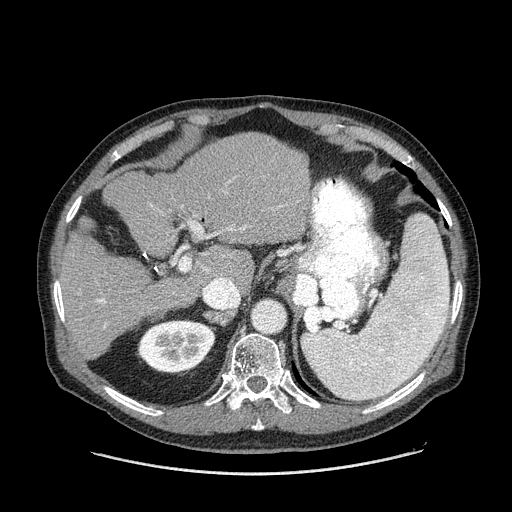
Contrast-enhanced abdominal CT (liver protocol), one axial slice. Slice 94 of 180 in the series (ordered by position). Reconstruction kernel STANDARD. 120 kVp. One of 2 acquisitions stored at this slice position. Soft-tissue window (W 400 / L 40 HU). 2.5 mm slice thickness. 512 × 512 image matrix, field of view 420 × 420 mm. Case-level facts recorded for this patient, not image findings: diagnosis: hepatocellular carcinoma (patient treated with transarterial chemoembolisation; whether this scan precedes or follows treatment is not stated here); TNM stage (as recorded): Stage-II; Child-Pugh class: A; tumour differentiation: well differentiated; tumour nodularity: multinodular.
Structures marked on this image (semi-automatic segmentation, software-assisted and operator-edited):
- liver parenchyma outside the tumour (the mass and vessels are separate outlines, so this box may not span the whole liver): bounding box <58,132,312,358> (left, top, right, bottom; pixels)
- liver vessels: <97,192,299,327>